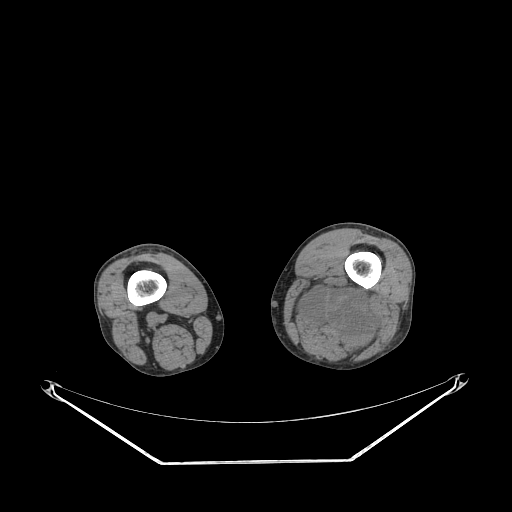
CT of an extremity soft-tissue mass (from a PET/CT study), one axial slice. Slice 207 of 267 in the series (ordered by position). Reconstruction kernel STANDARD. 140 kVp. Soft-tissue window (W 400 / L 40 HU). 512 × 512 image matrix, field of view 500 × 500 mm. Male patient. From the clinical record (not read from this slice): histological type: undifferentiated pleomorphic liposarcoma; grade: high; site of the primary tumour: left thigh.
Outlined on this slice (expert contour drawn on MRI and transferred to this co-registered scan by the dataset authors):
- gross tumour volume including surrounding oedema: bounding box (x1, y1, x2, y2) in pixels: (292, 276, 376, 357)
- gross tumour volume (mass): (304, 295, 366, 337)